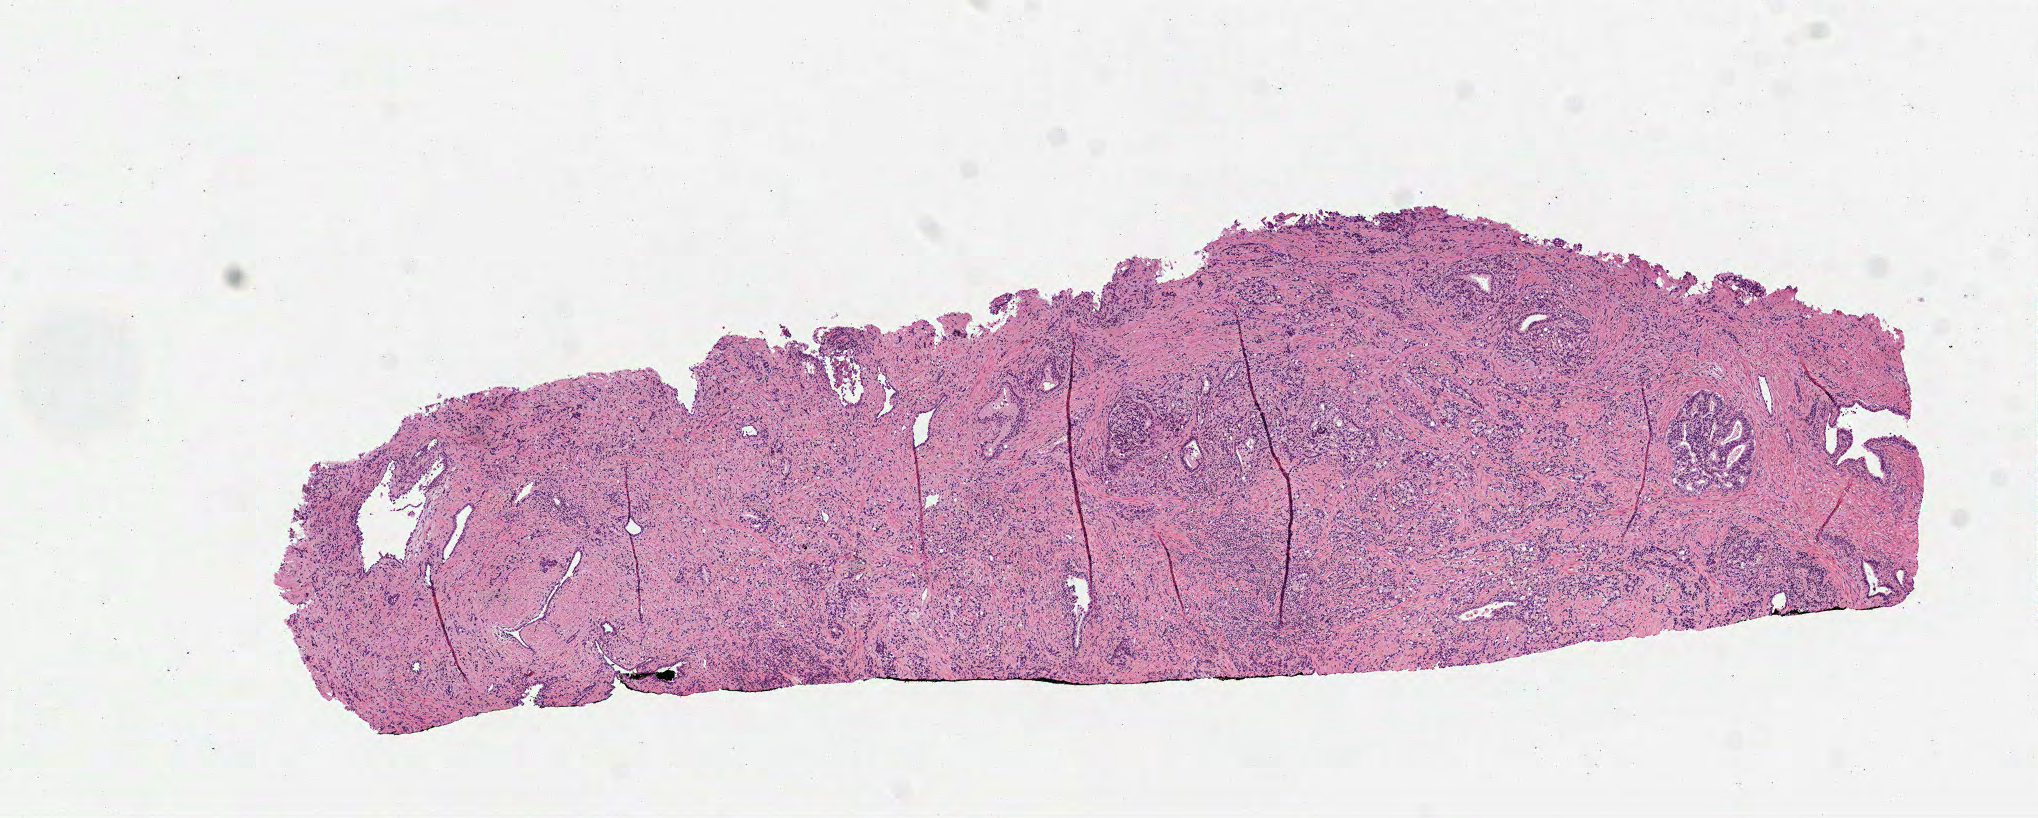
Hematoxylin and eosin (H&E) stained whole-slide image, whole scanned area (about 8.2 x 3.3 mm) shown as a low-resolution overview, formalin-fixed paraffin-embedded (FFPE) diagnostic section, sample: primary tumour, prostate. Male, age 55 years at initial diagnosis. Gleason score: 8 (4+4).
Pathologic diagnosis: Acinar cell carcinoma (prostate gland). Laterality: bilateral.